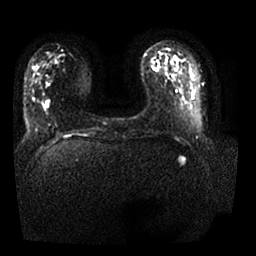
Breast MRI, one axial slice. Slice 8 of 25 in the series (ordered by position). Diffusion-weighted series; image 2 of 4 stored at this slice position (different b-values; order by instance number). 1.5 T. 4 mm slice thickness. 256 × 256 image matrix, field of view 350 × 350 mm. Female patient.
Annotated regions visible in this slice (outlined manually by an expert reader):
- tumour on diffusion-weighted imaging: bounding box <44,102,48,108> (left, top, right, bottom; pixels)